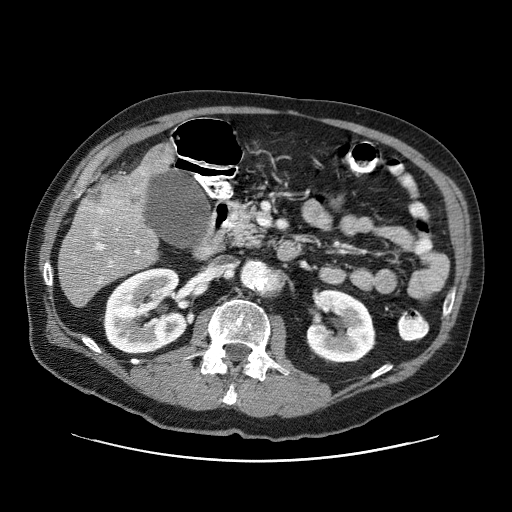
Contrast-enhanced abdominal CT (liver protocol), one axial slice; position 23 of 87 along the scan axis; one of 3 acquisitions stored at this slice position; soft-tissue window (W 400 / L 40 HU); 512 × 512 image matrix, field of view 400 × 400 mm. From the clinical record (not read from this slice): diagnosis: hepatocellular carcinoma (patient treated with transarterial chemoembolisation; whether this scan precedes or follows treatment is not stated here); TNM stage (as recorded): Stage-IIIA; Child-Pugh class: A; tumour differentiation: well differentiated; tumour nodularity: multinodular.
Outlined on this slice (semi-automatic segmentation, software-assisted and operator-edited):
- liver parenchyma outside the tumour (the mass and vessels are separate outlines, so this box may not span the whole liver): bounding box (x1, y1, x2, y2) in pixels: (58, 144, 174, 307)
- mass: (75, 171, 146, 234)
- liver vessels: (93, 172, 144, 283)